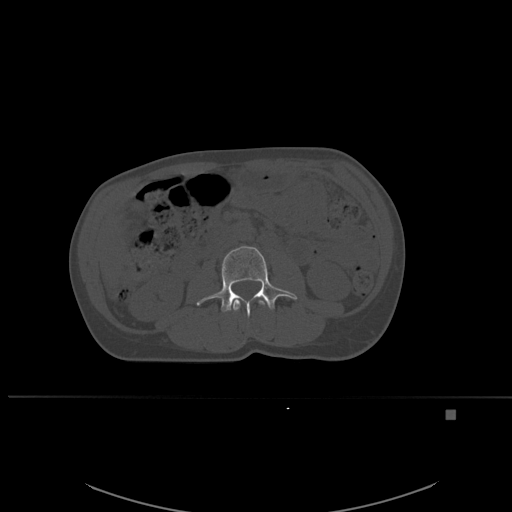
CT including the spine, one axial slice; position 218 of 537 along the scan axis; bone window (W 1800 / L 400 HU); 1.5 mm slice thickness; 512 × 512 image matrix, field of view 440 × 440 mm. Female patient, age 45 years. From the clinical record (not read from this slice): primary cancer: lung.
Structures marked on this image (semi-automatically segmented with operator editing):
- L2 vertebra: bounding box <233,297,268,312> (left, top, right, bottom; pixels)
- L3 vertebra: <196,246,297,317>